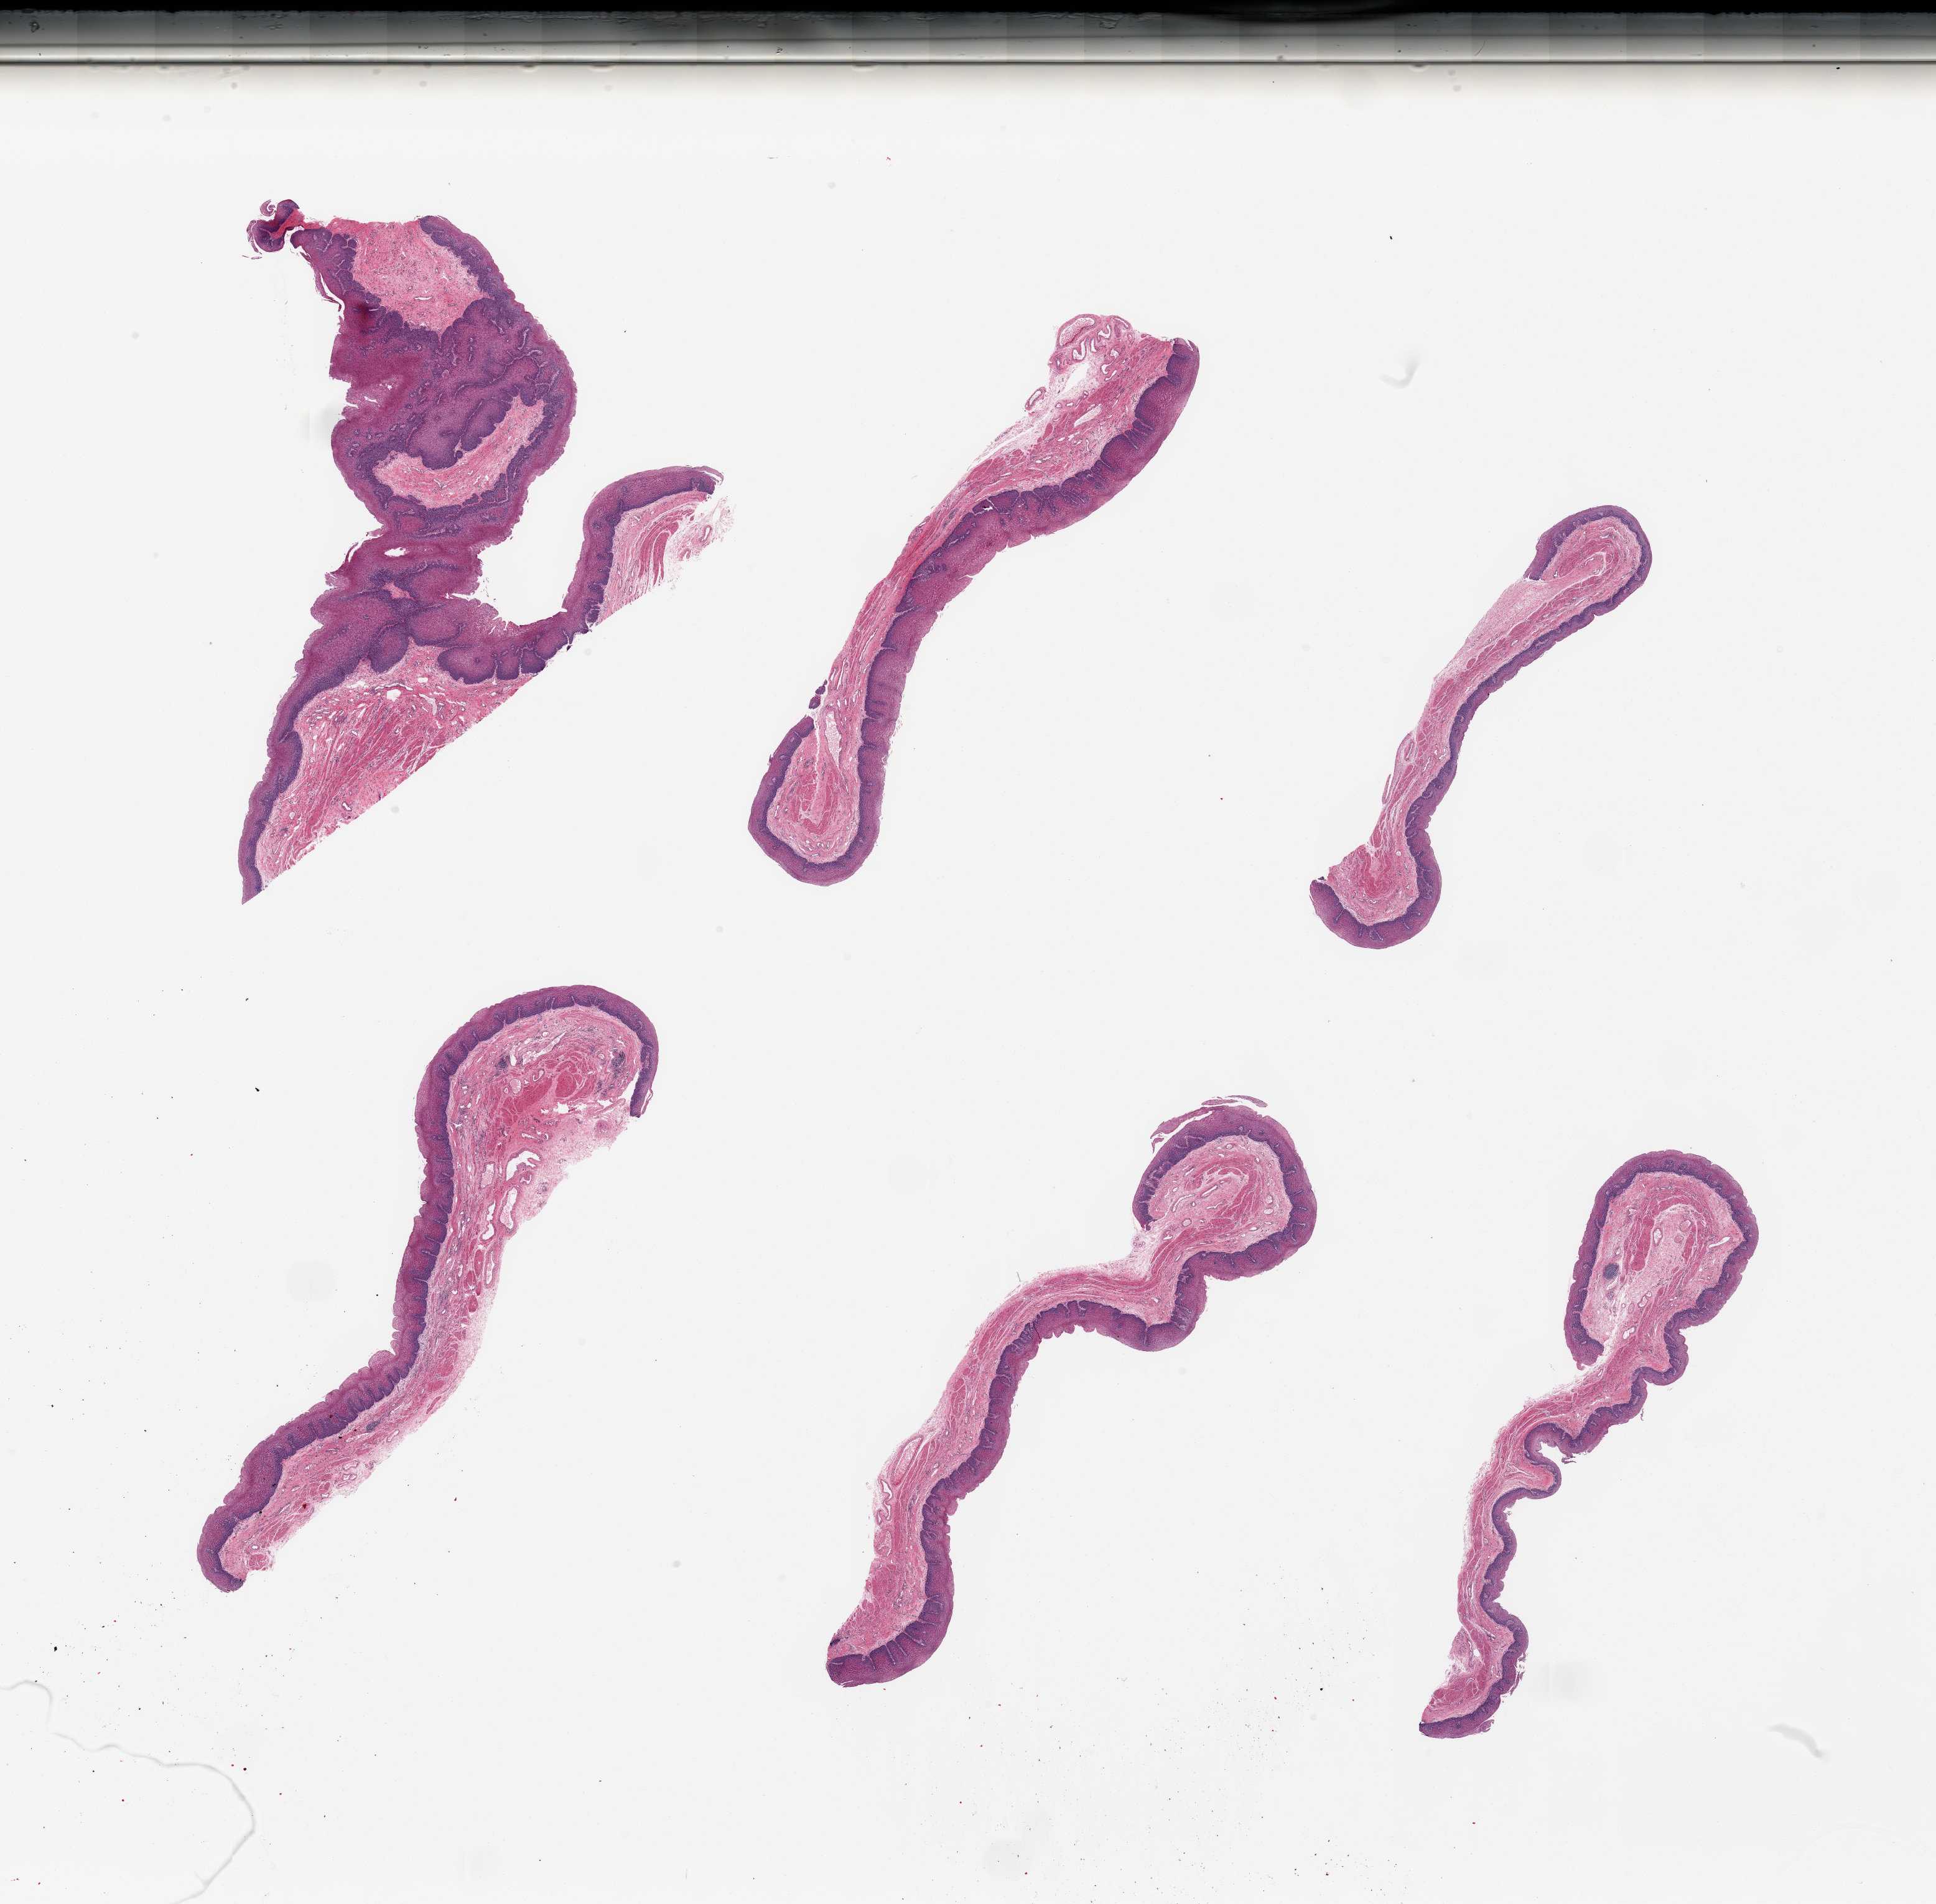
Whole-slide image, hematoxylin and eosin (H&E) stain — shown as a low-resolution overview of the whole scanned area (about 24.6 x 24.2 mm, acquisition: 20x scan); PAXgene-fixed, paraffin-embedded tissue; target tissue: esophageal mucous membrane; tissue donor sample. Donor sex: male.
Review note (as recorded): 6 pieces; well dissected; slight surface desquamation.